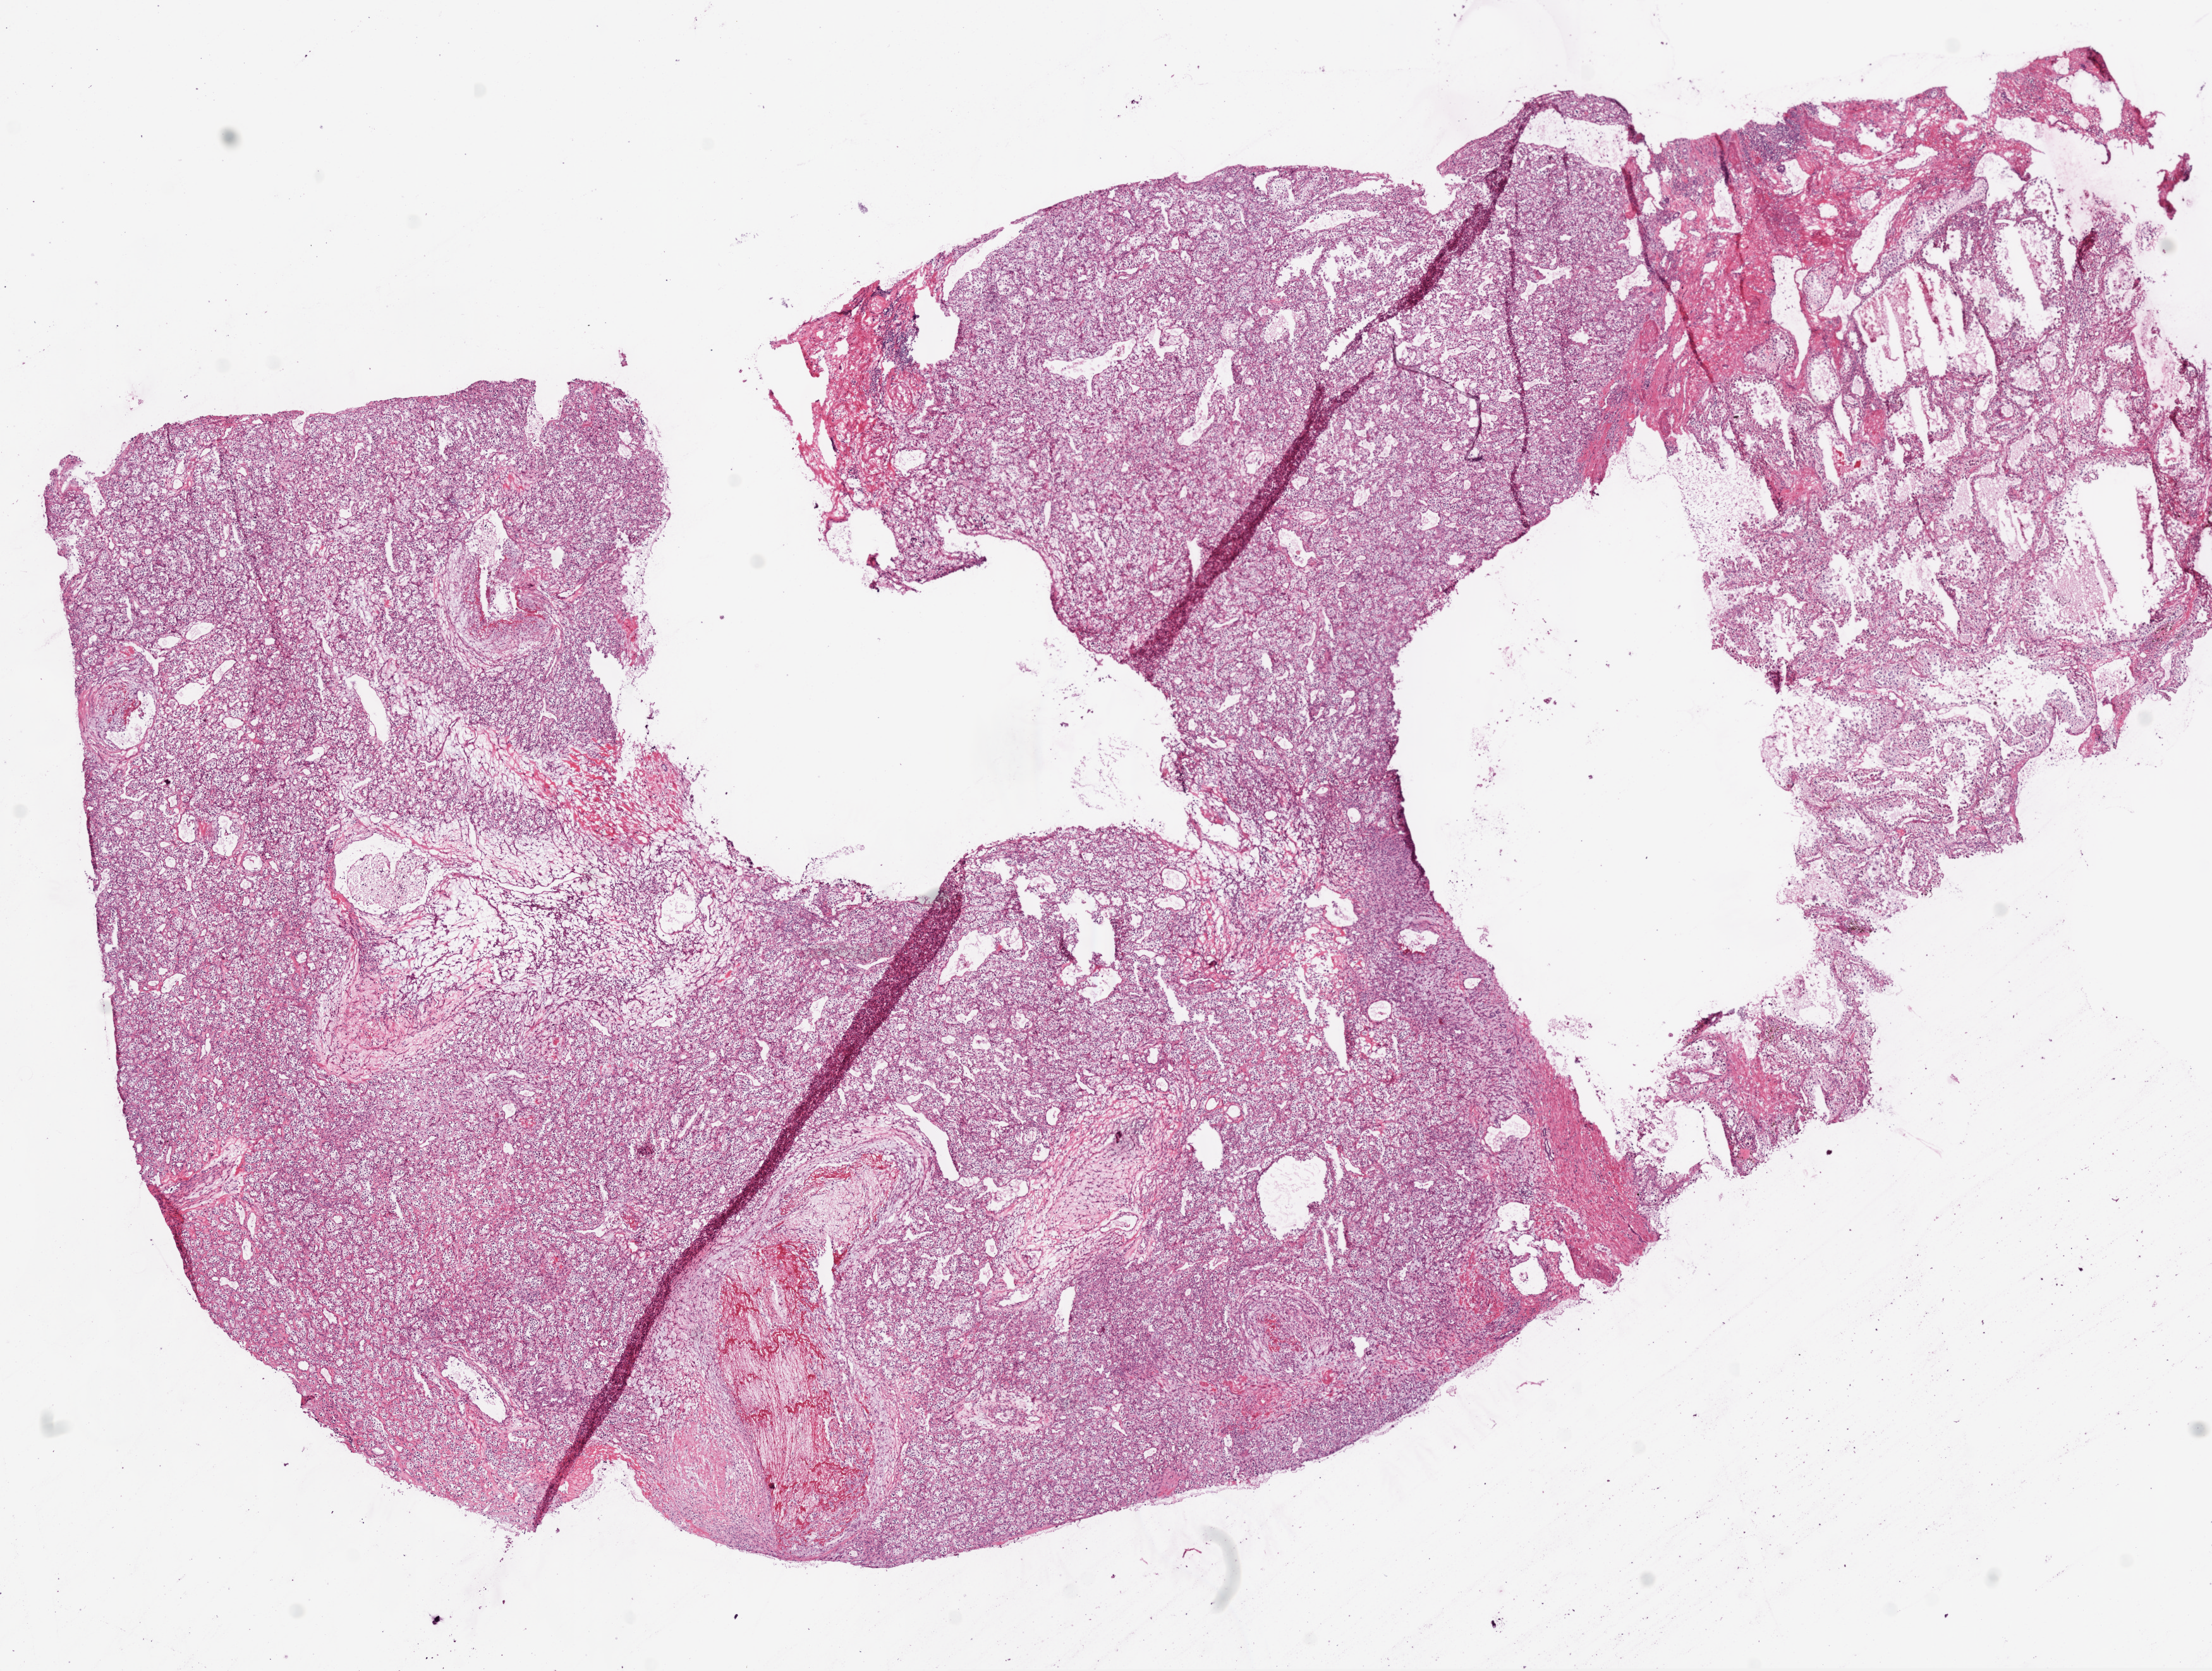
Digitized H&E tissue section (whole slide), a low-resolution overview of the entire scanned area, about 14.0 x 10.6 mm (slide scanned at 20x); frozen section from the bottom of the tissue portion; primary tumour sample from the kidney. Male, age 69 years at initial diagnosis. Histologic grade: G3 (poorly differentiated). Pathologist review of this section (percent, as recorded): tumour cells 70%, tumour nuclei 80%, normal cells 20%, stromal cells 10%, necrosis 0%.
* lymph nodes positive (case pathology): 0 of 10 examined
* AJCC pathologic stage: III
* diagnosis: Clear cell adenocarcinoma, NOS